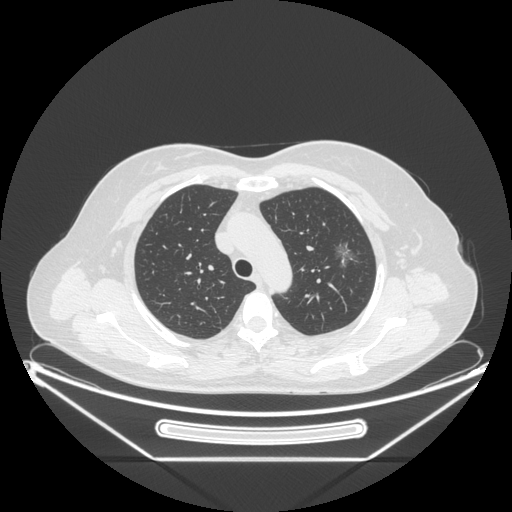
Chest CT, one axial slice. Position 164 of 226 along the scan axis. Reconstruction kernel STANDARD. Lung window (W 1500 / L -600 HU). 512 × 512 image matrix, field of view 447 × 447 mm. Patient: female, 54 years. From the clinical record (not read from this slice): clinical TNM (as recorded): T1c N0 M0.
Annotated regions visible in this slice (bounding box drawn by a radiologist):
- lung tumour (recorded histology: adenocarcinoma): bounding box <331,236,363,276> (left, top, right, bottom; pixels)